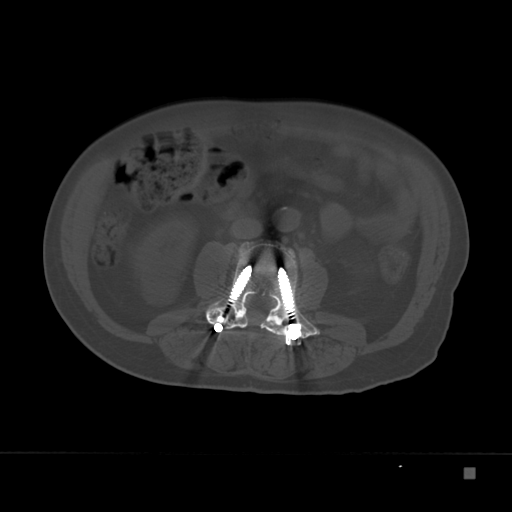
CT including the spine, one axial slice; position 69 of 332 along the scan axis; 120 kVp; bone window (W 1800 / L 400 HU); 1.5 mm slice thickness; 512 × 512 image matrix. Male patient, age 72 years. From the clinical record (not read from this slice): primary cancer: skeletal.
Annotated regions visible in this slice (semi-automatically segmented with operator editing):
- L3 vertebra: bounding box (x1, y1, x2, y2) in pixels: (205, 242, 322, 340)